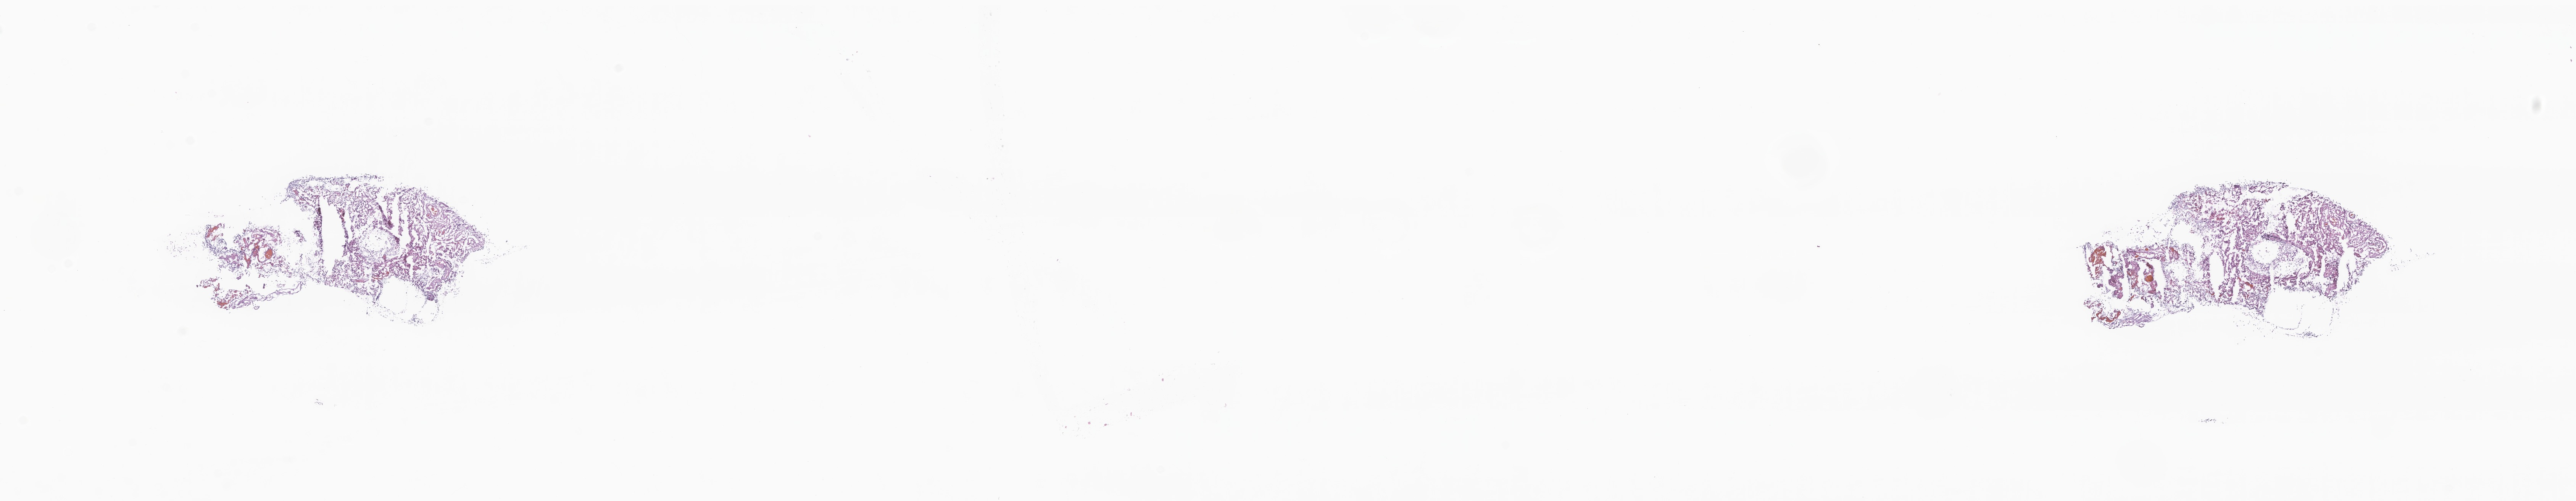
Digitized H&E-stained section of tumor tissue from the brain — shown as a low-resolution overview of the whole scanned area (about 28.5 x 5.5 mm); frozen section (OCT-embedded). Patient: male, age 37 months (3 years 1 month).
Diagnosis: Medulloblastoma, NOS.